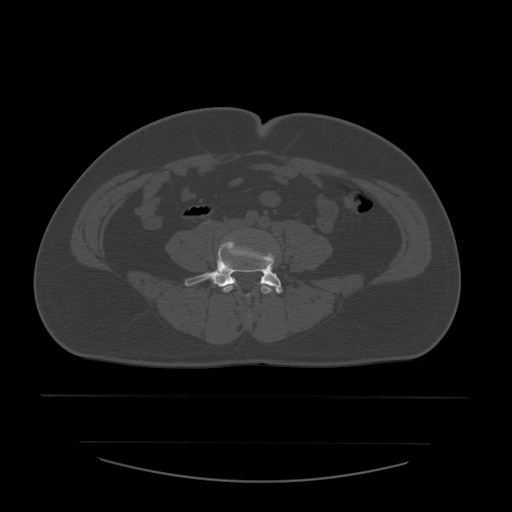
CT including the spine, one axial slice. Slice 129 of 532 in the series (ordered by position). 120 kVp. Bone window (W 1800 / L 400 HU). 512 × 512 image matrix, field of view 441 × 441 mm. Patient age 44 years. Case-level facts recorded for this patient, not image findings: primary cancer: soft tissue sarcoma.
Structures marked on this image (semi-automatic segmentation, software-assisted and operator-edited):
- L4 vertebra: bounding box <223,285,273,318> (left, top, right, bottom; pixels)
- L5 vertebra: <184,242,283,294>